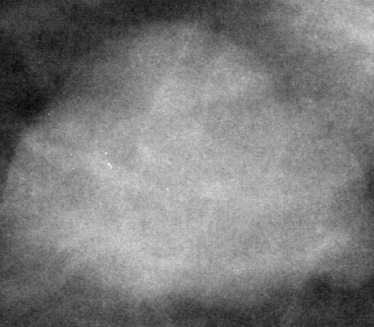
Cropped region of a digitized screen-film mammogram centred on a radiologist-marked abnormality, left breast, CC view, BI-RADS breast density category 2 (scale 1–4).
Finding: mass, shape lobulated, margins circumscribed; BI-RADS assessment category 3; pathology result (as recorded, not read from the image): benign.